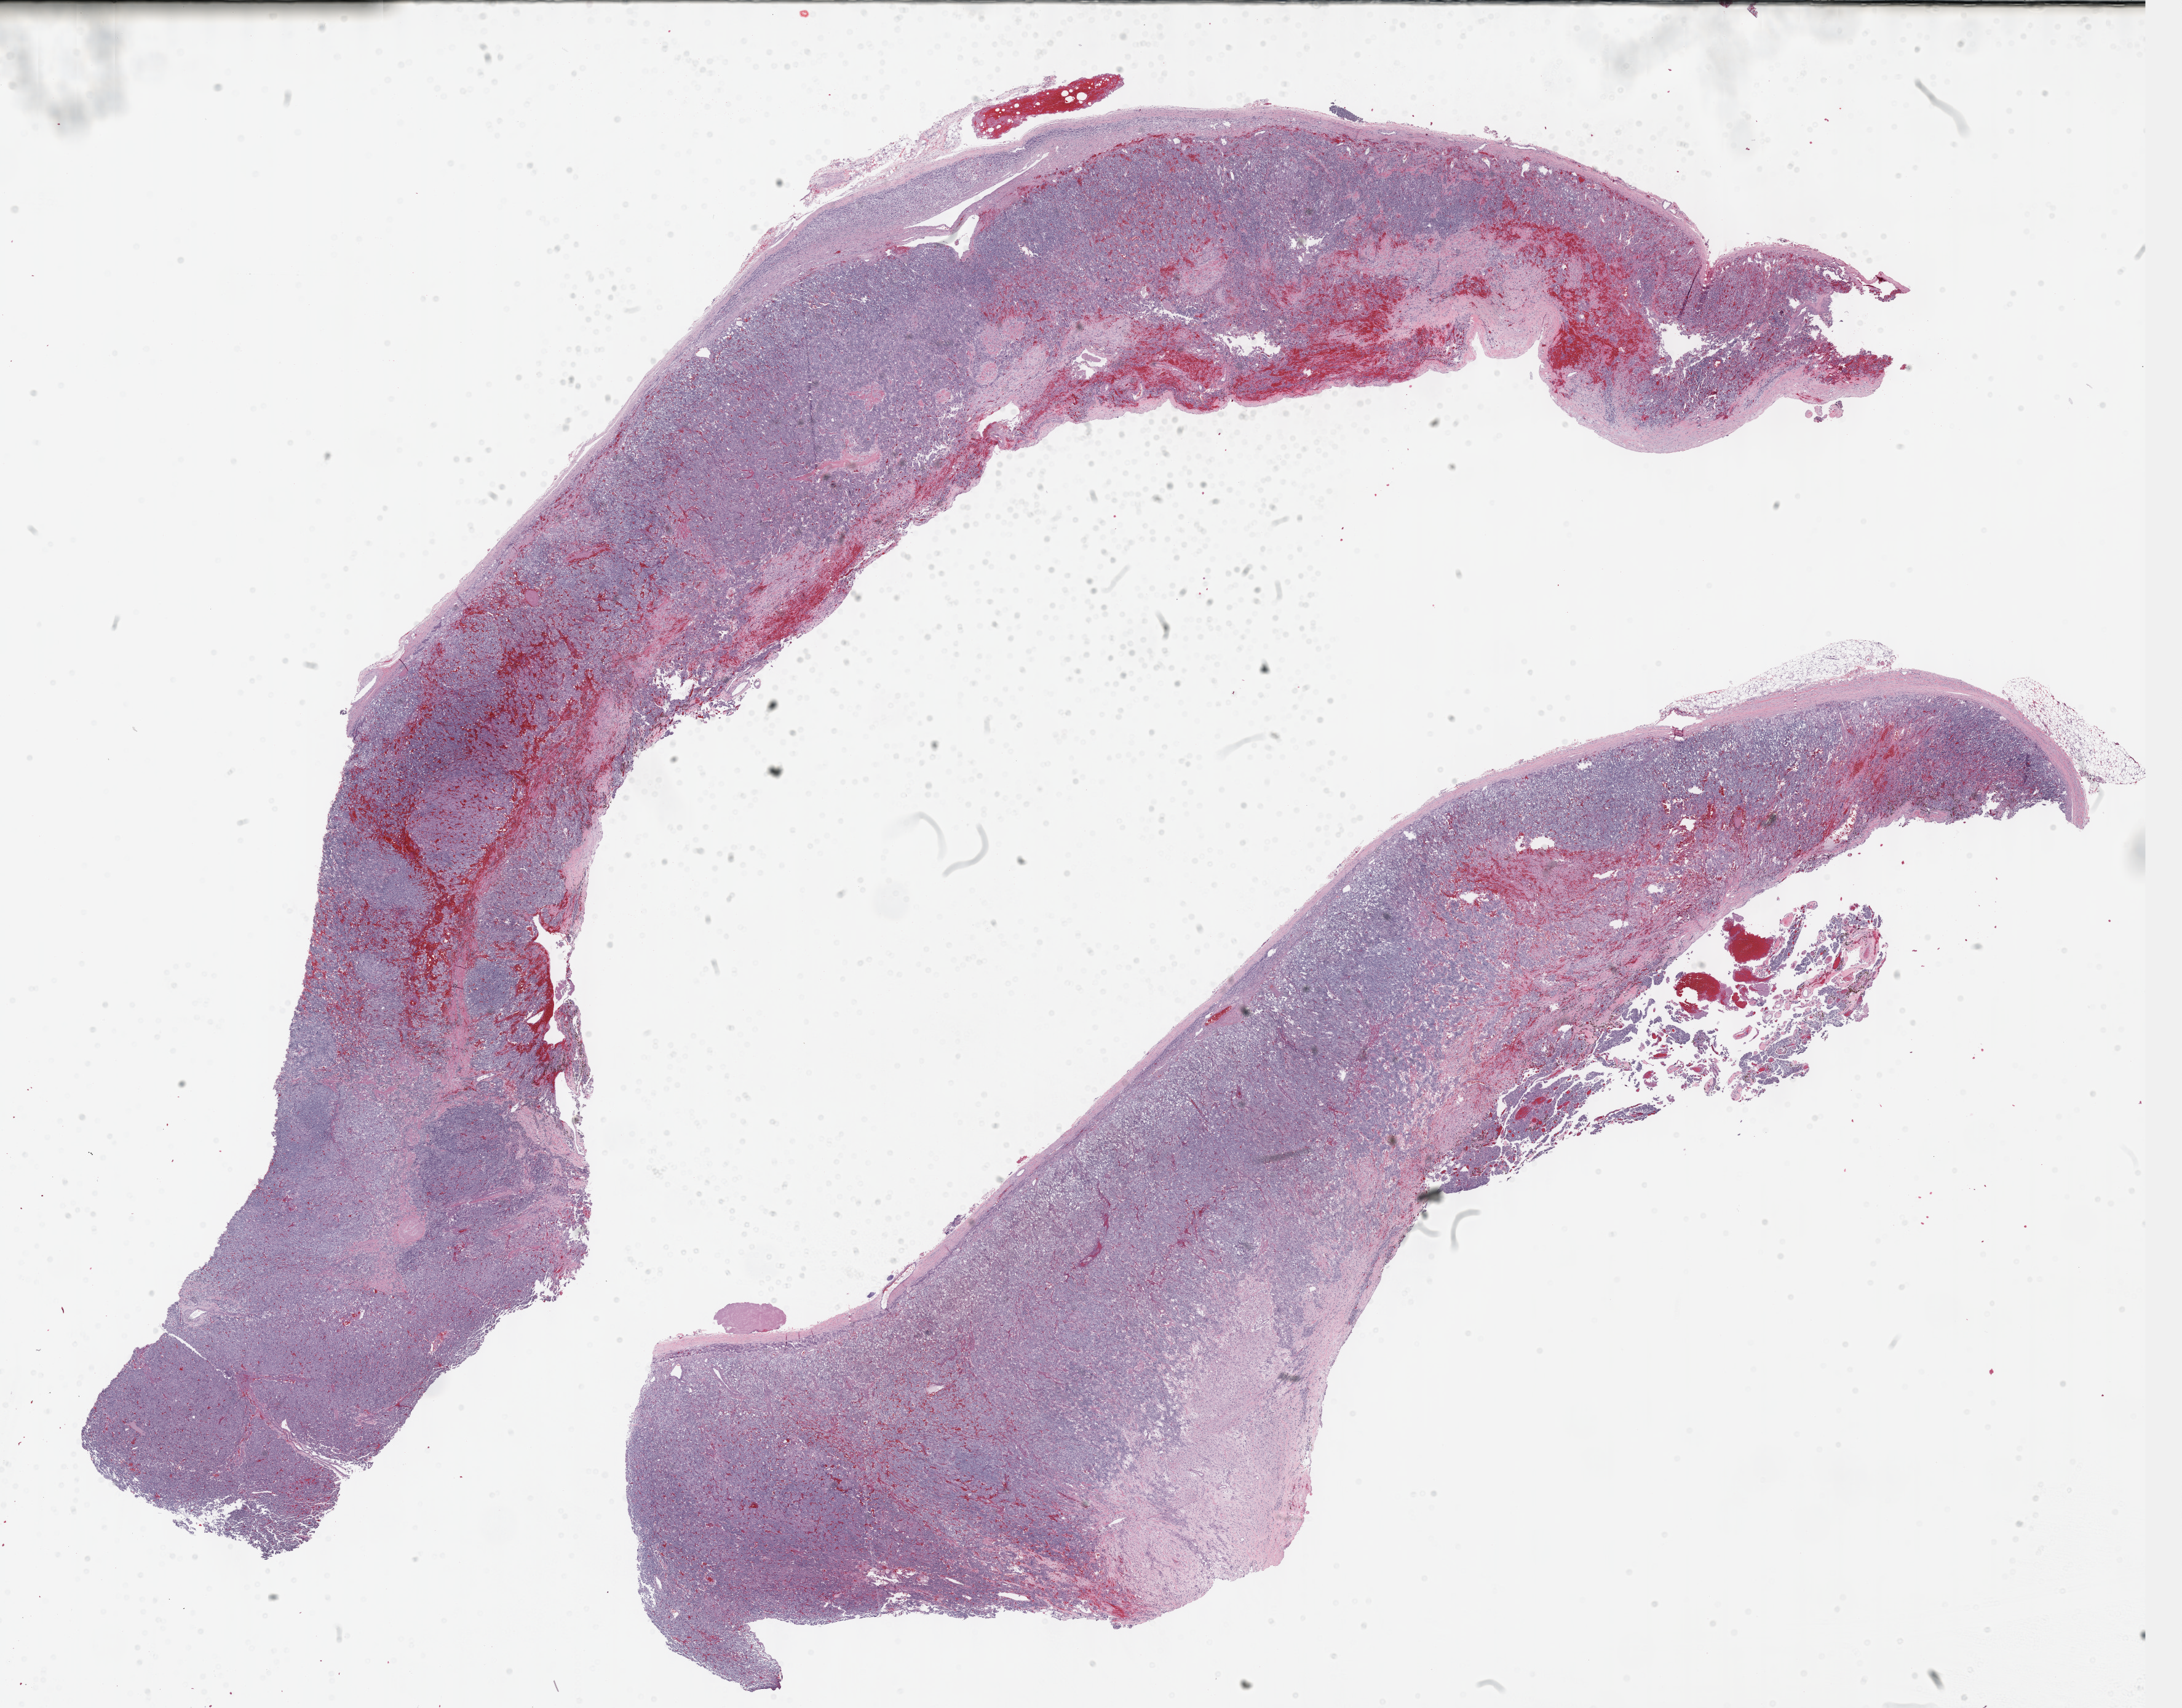
H&E-stained whole-slide image, whole scanned area (about 28.7 x 22.4 mm, slide scanned at 40x) shown as a low-resolution overview. Formalin-fixed paraffin-embedded (FFPE) diagnostic section. Sample: primary tumour, adrenal gland. Patient: female, age at initial diagnosis 54 years.
Diagnosis: Pheochromocytoma, NOS.